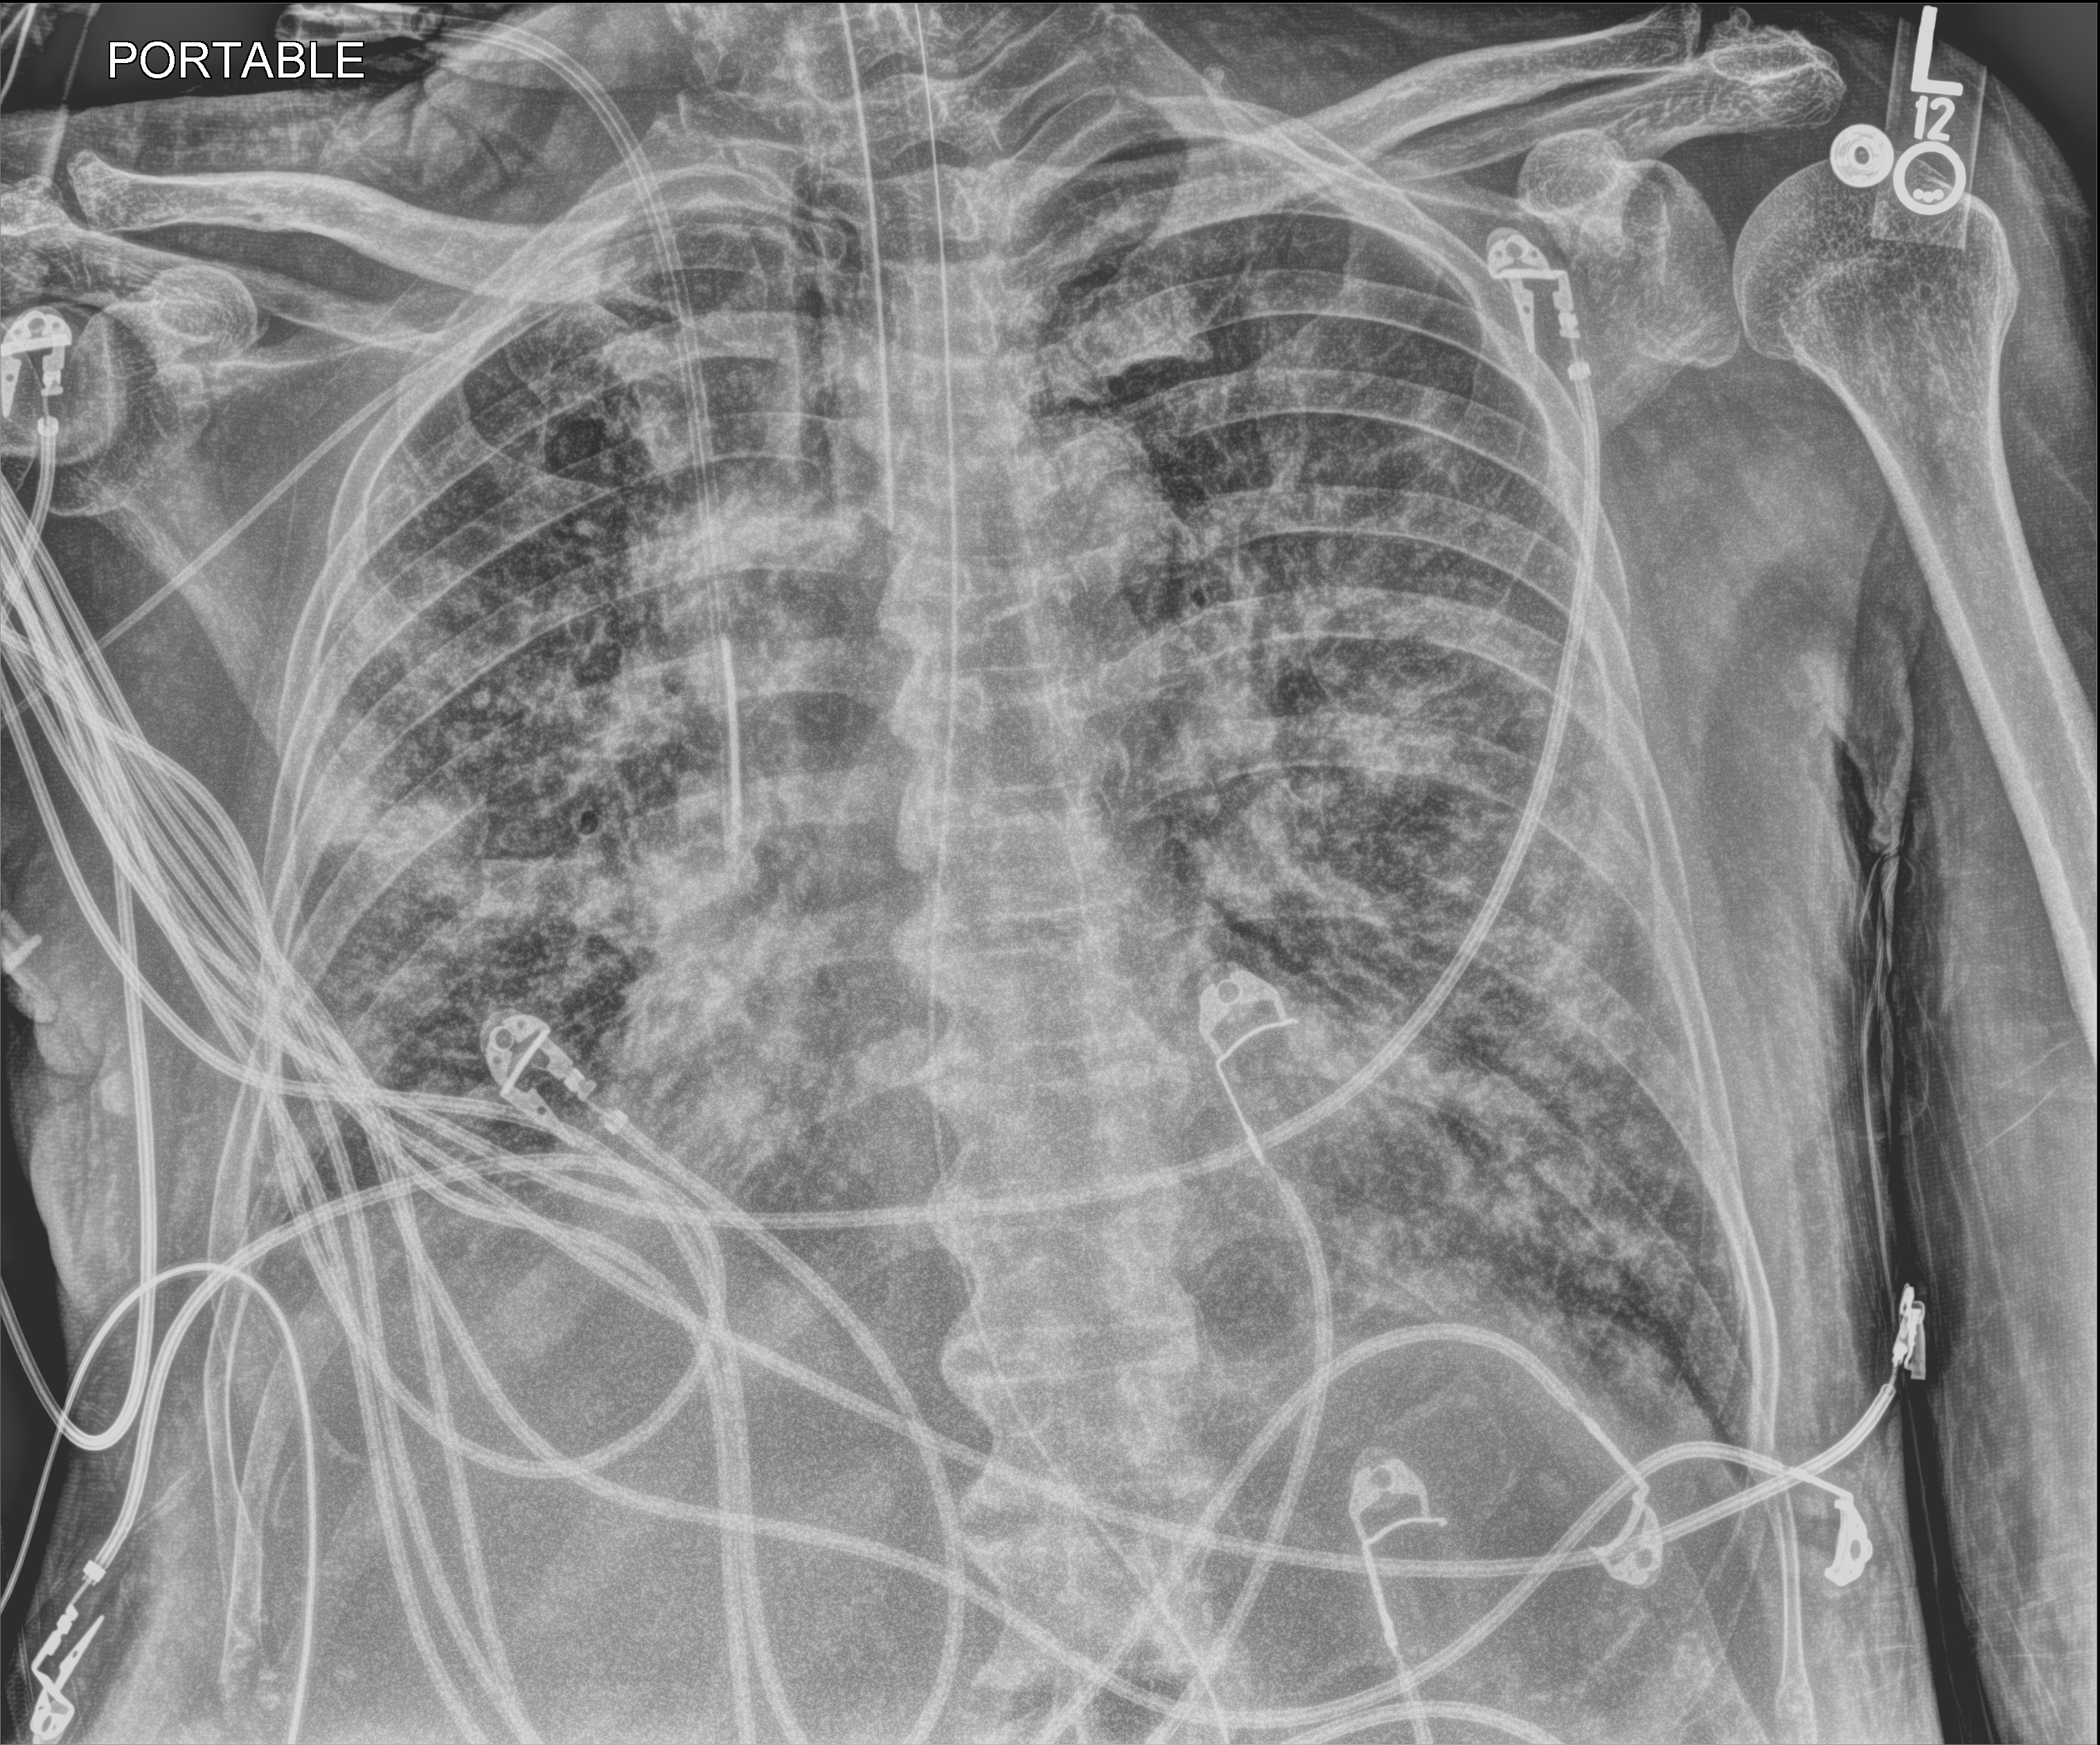
Chest X-ray (portable). Patient hospitalised with COVID-19; male, aged 60–74 years.
Admission-level facts for this patient (not findings on this image; timing relative to this image not recorded): COPD (admission record): no; mechanically ventilated during this hospital stay: yes; admitted to intensive care during this hospital stay: yes.